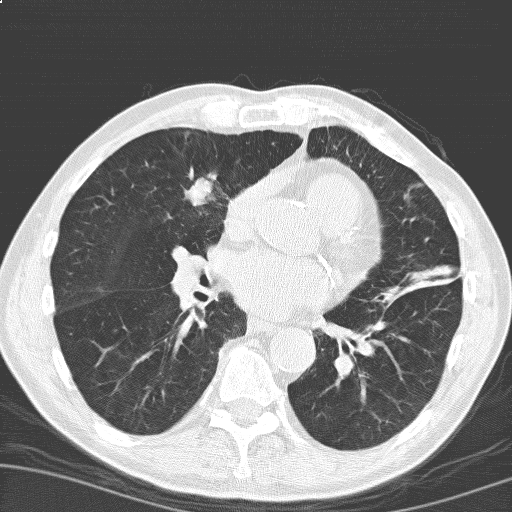
Low-dose screening chest CT, one axial slice. Slice 90 of 184 in the series (ordered by position). Lung window (W 1500 / L -600 HU). 3.2 mm slice thickness. 512 × 512 image matrix, field of view 329 × 329 mm.
Outlined on this slice (outlined manually by an expert reader):
- lesion 1 (tumor, upper lobe of right lung): bounding box [x1, y1, x2, y2] px = [186, 174, 216, 206]